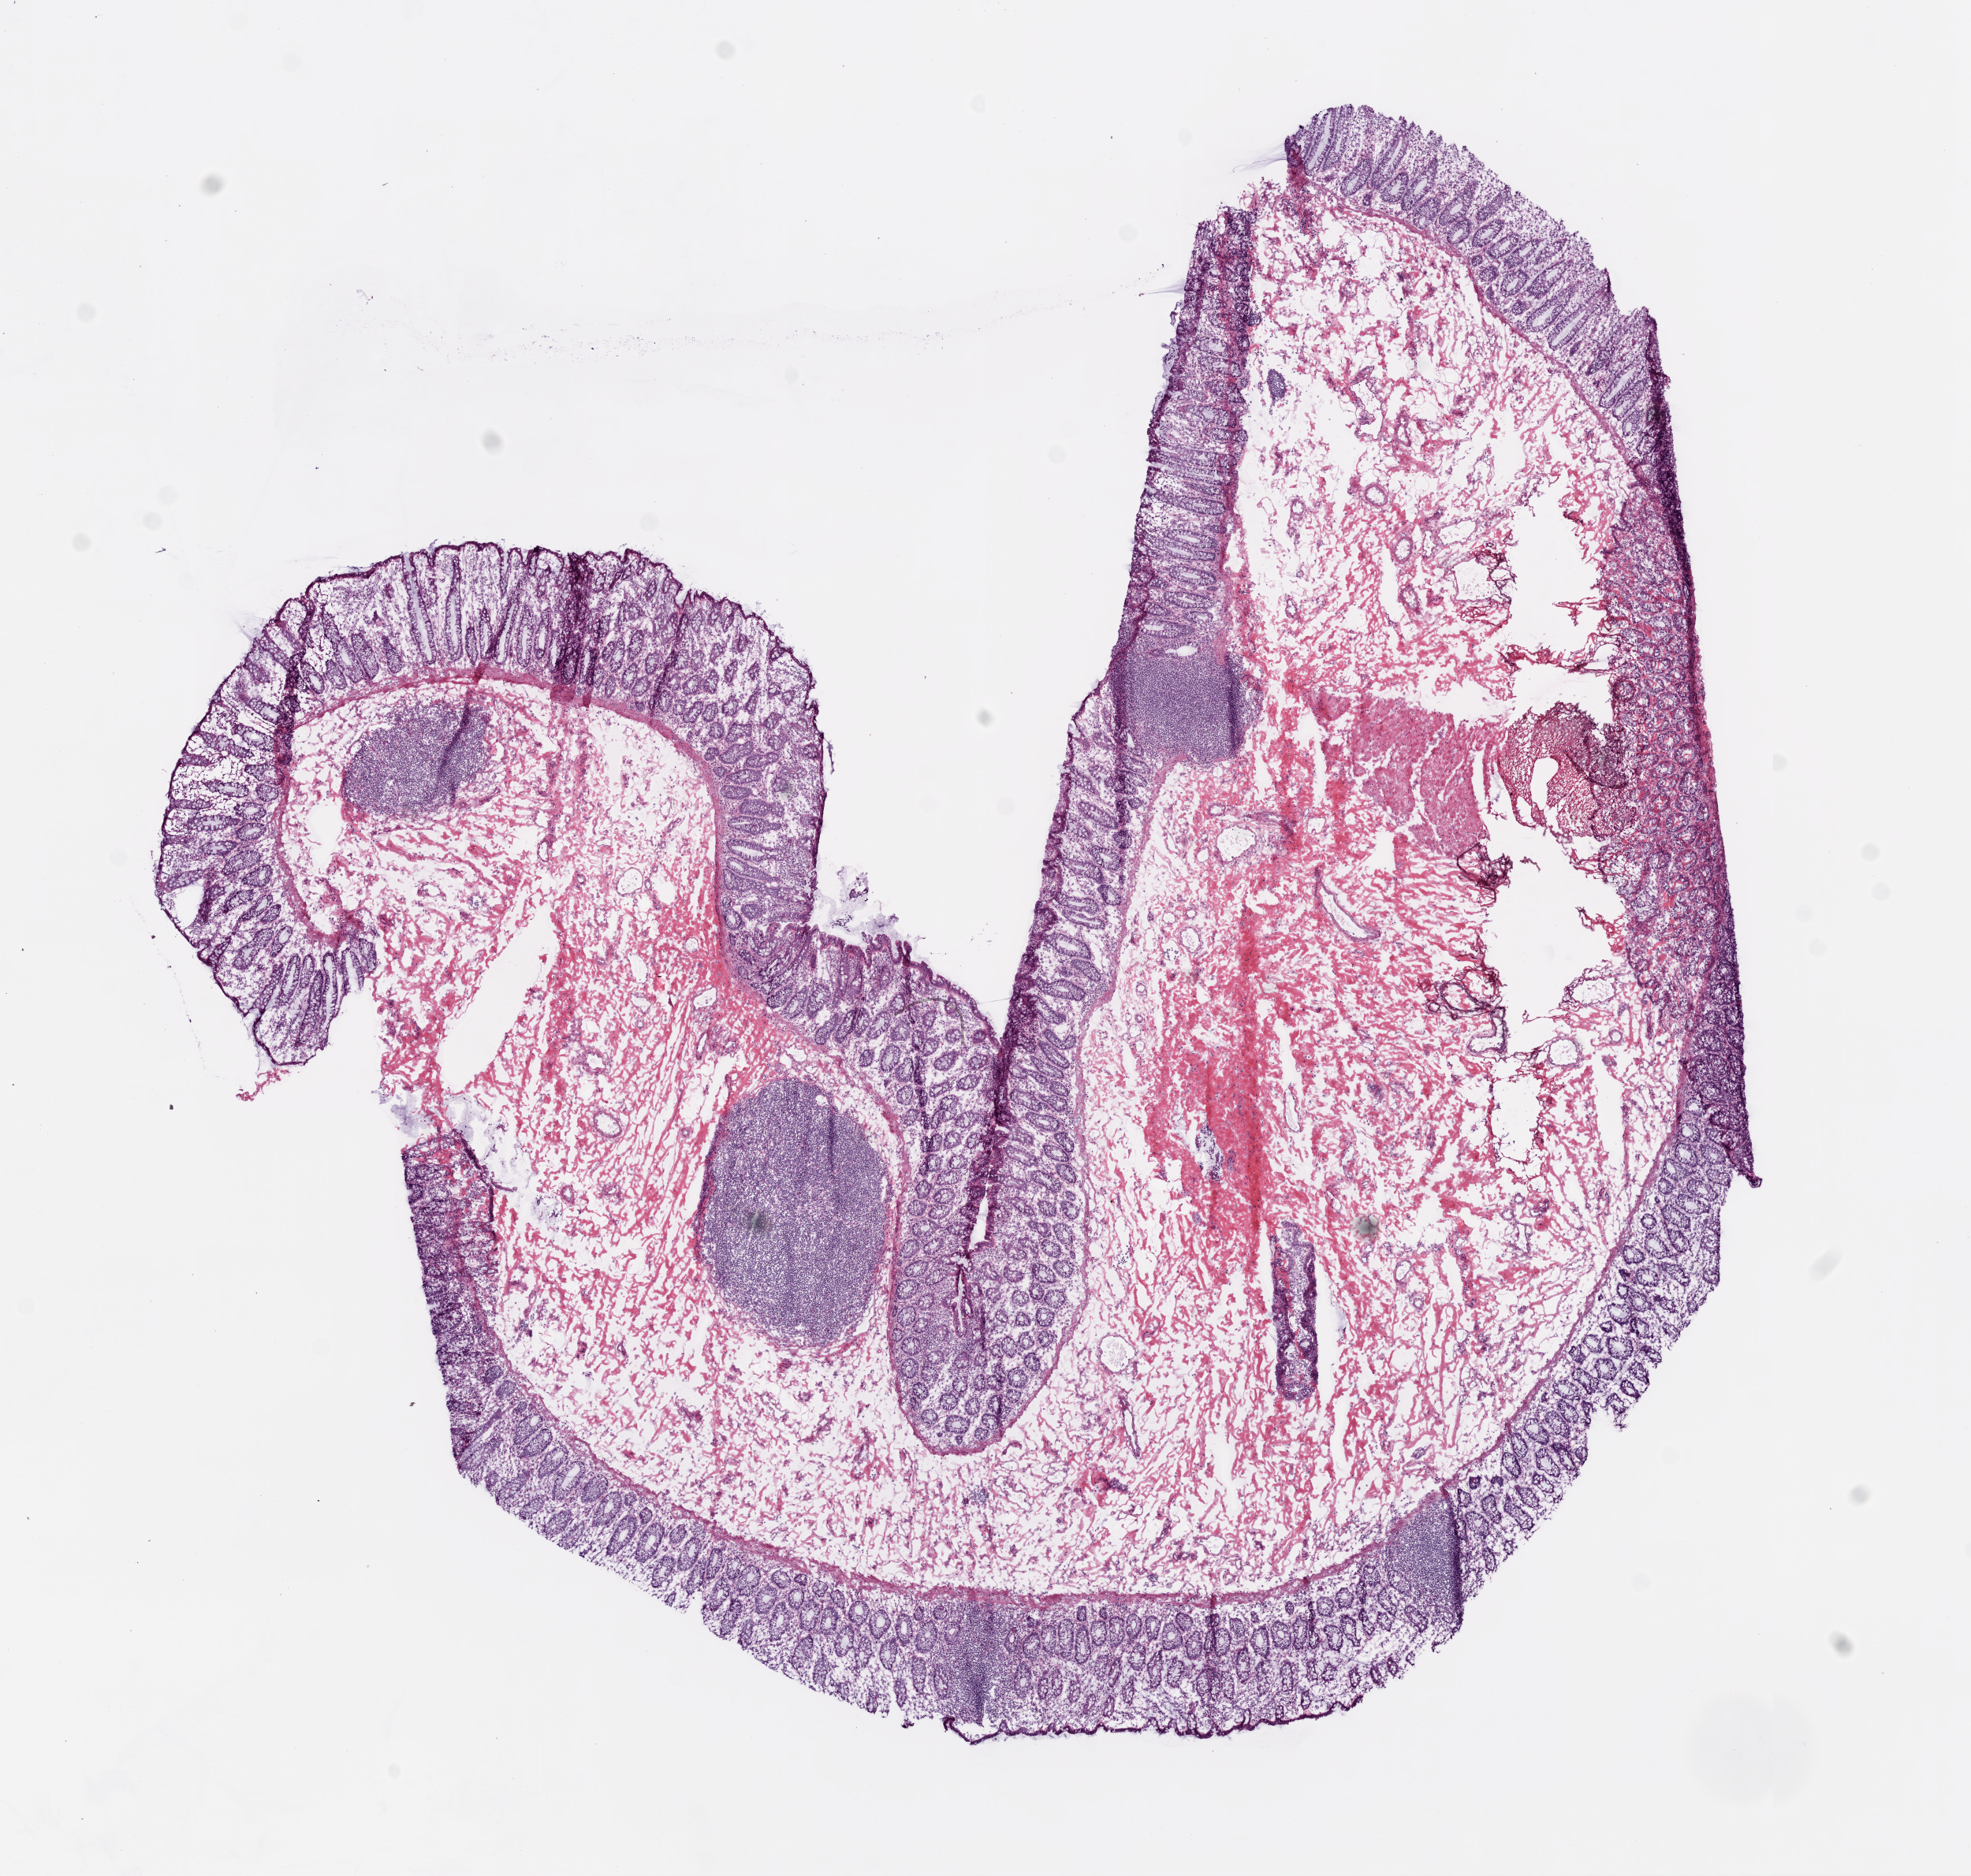
Whole-slide histology image, H&E — low-resolution overview of the scanned area, about 10.0 x 9.5 mm, frozen section from the top of the tissue portion, colon, solid tissue normal (non-tumour tissue) sample. Male patient; age at initial diagnosis 55 years.
• this section: solid tissue normal (non-tumour) sample from the same patient
• patient diagnosis: Adenocarcinoma, NOS